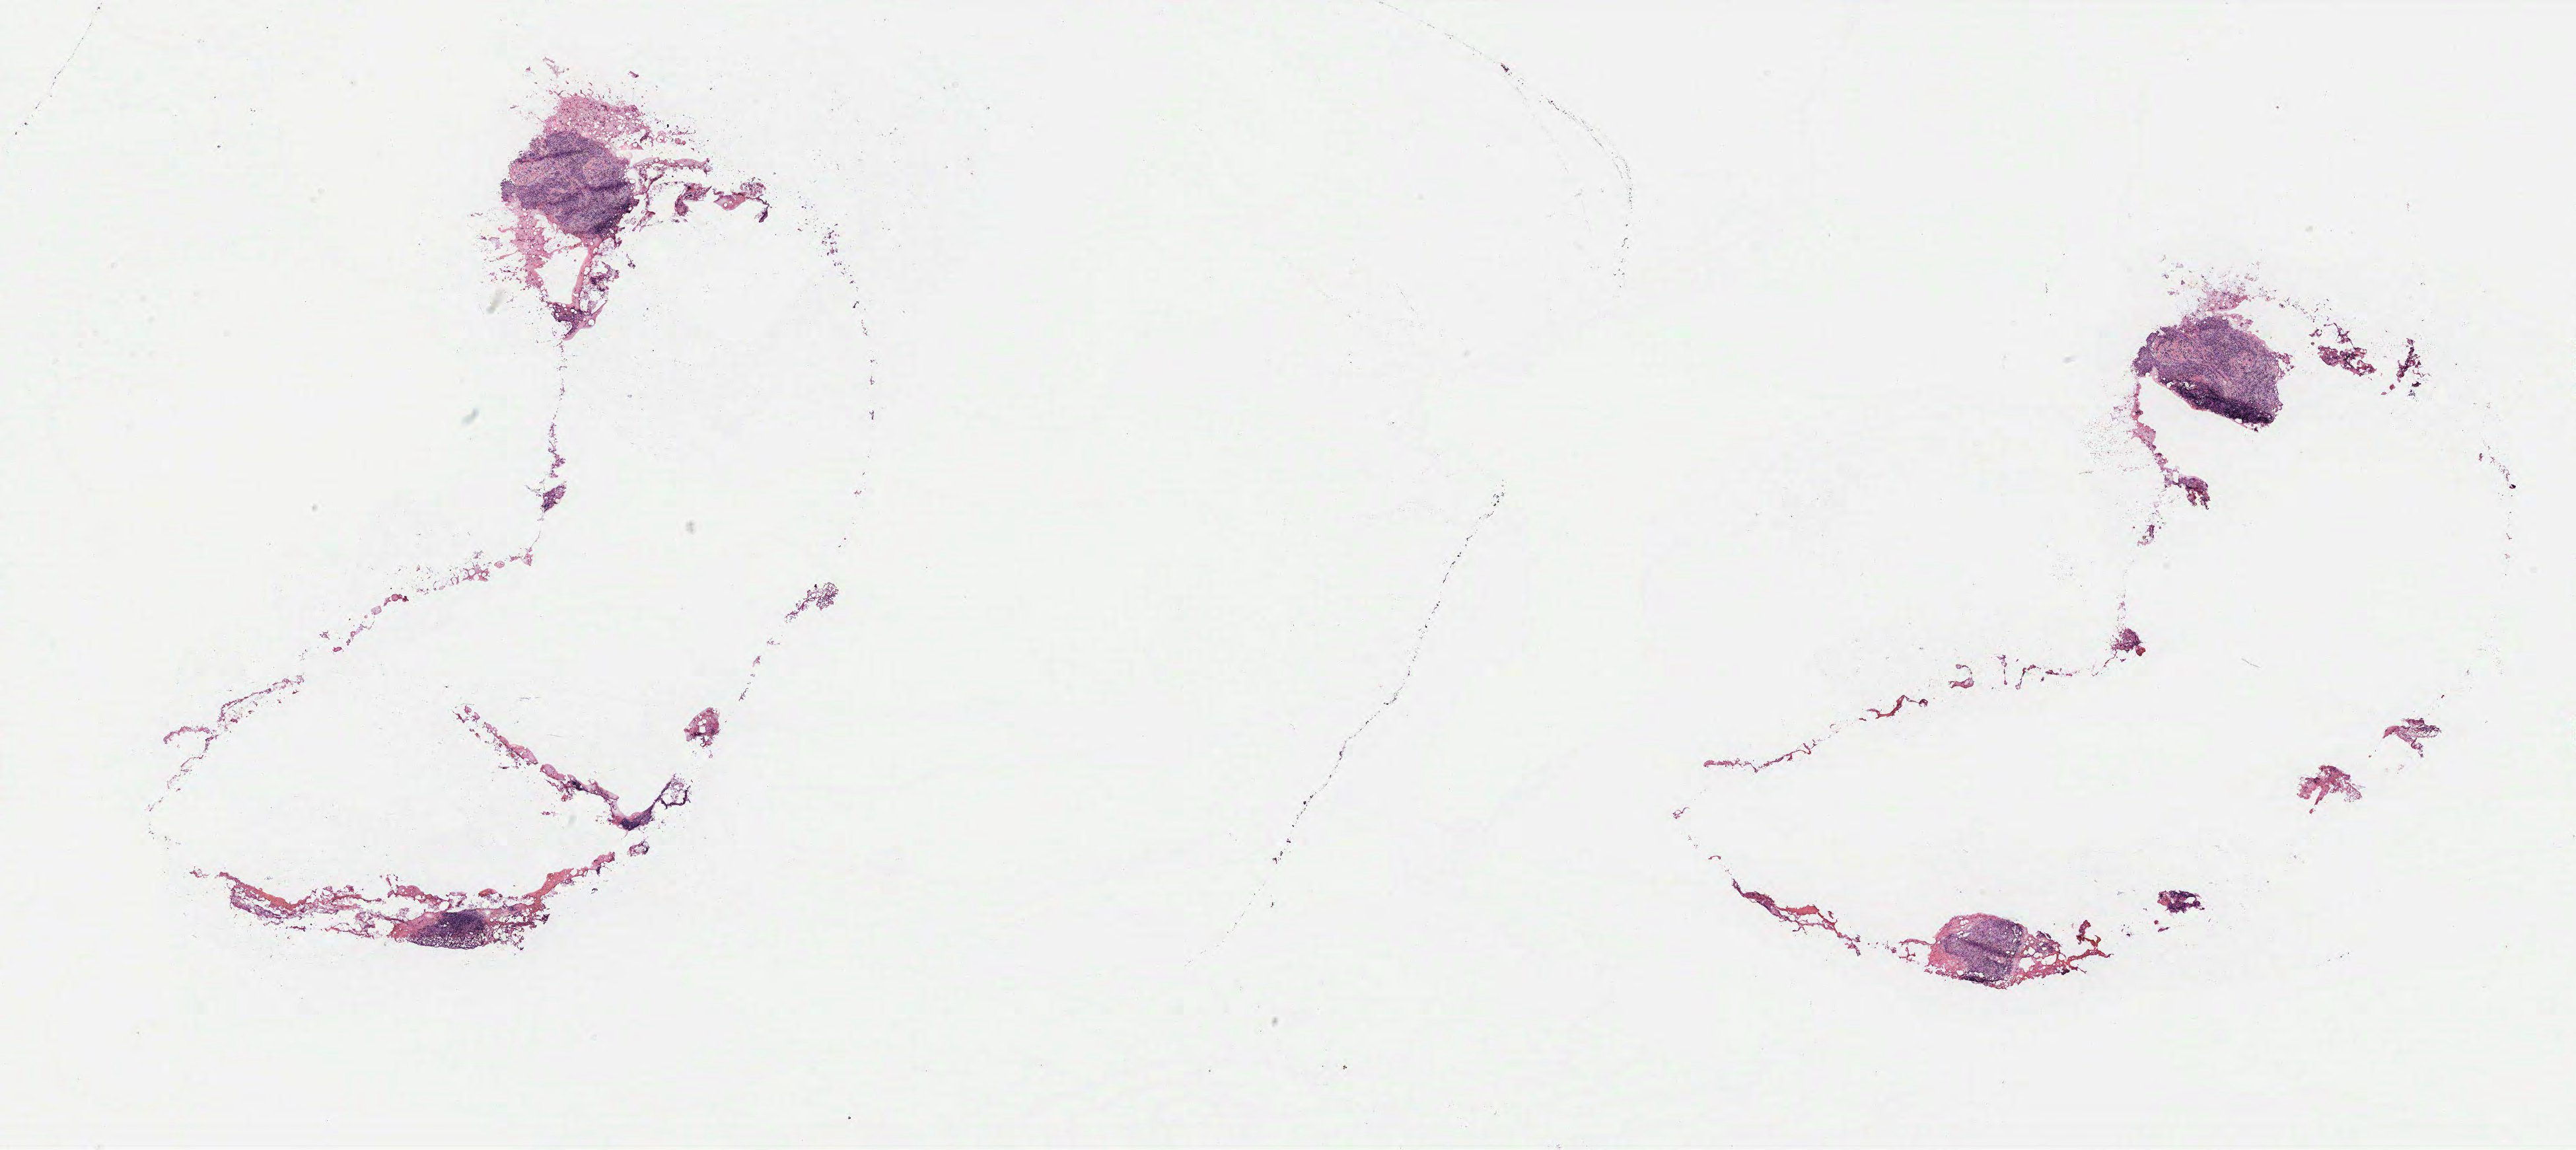
Digitized Hematoxylin and eosin (H&E) stained tissue section (whole slide) — shown as a low-resolution overview of the whole scanned area (about 31.2 x 13.9 mm, from a 40x scan), breast, tissue type not recorded.
* patient diagnosis (cohort enrolment): breast cancer (breast)